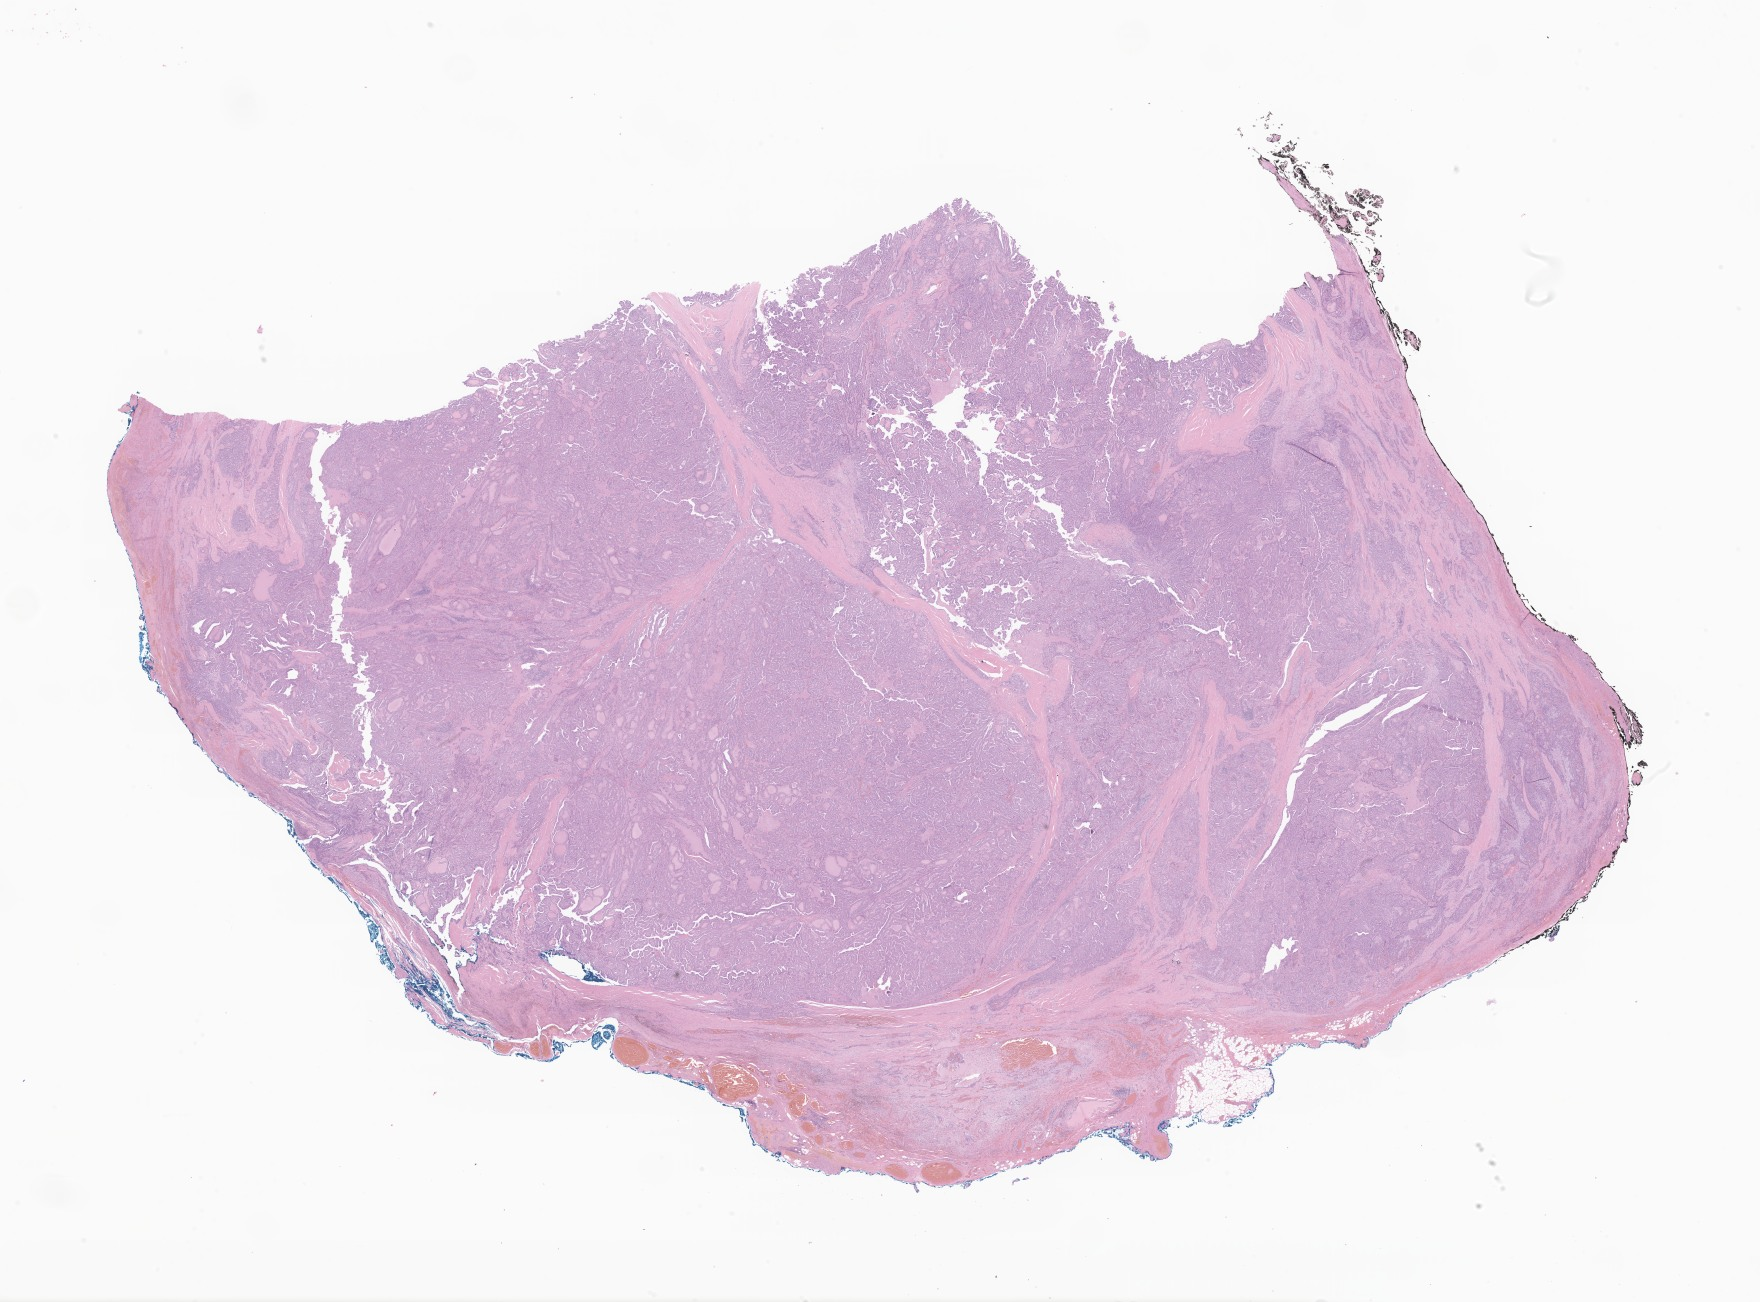
Whole-slide image, hematoxylin and eosin (H&E) stain of tumor tissue from the thyroid, whole scanned area (about 29.7 x 22.0 mm) shown as a low-resolution overview. Formalin-fixed, paraffin-embedded (FFPE) tissue. Patient female; age 192 months.
Diagnosis (ICD-O-3 morphology term): Papillary carcinoma, NOS.